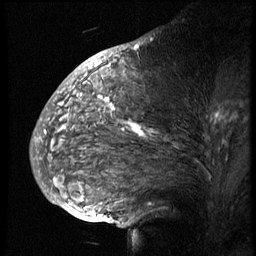
Breast MRI (dynamic contrast-enhanced), one sagittal slice. Slice 37 of 74 in the series (ordered by position). 3 images stored at this slice position (order not interpretable as contrast timing). 1.5 T. TE 4.2 ms, TR 8.9 ms. 2.5 mm slice thickness. 256 × 256 image matrix, field of view 200 × 200 mm. Patient: female, 57 years. From the clinical record (not read from this slice): setting: breast cancer imaged before/during neoadjuvant chemotherapy; receptor status: HER2-positive.
Outlined on this slice (semi-automatic segmentation, software-assisted and operator-edited):
- analysis volume of interest (the breast-tissue region the enhancement analysis was run in; not a lesion): bounding box [x1, y1, x2, y2] px = [51, 67, 249, 173]
- tumour enhancement mask (voxels above the 140 % enhancement threshold inside the analysis volume of interest): [100, 97, 223, 136]